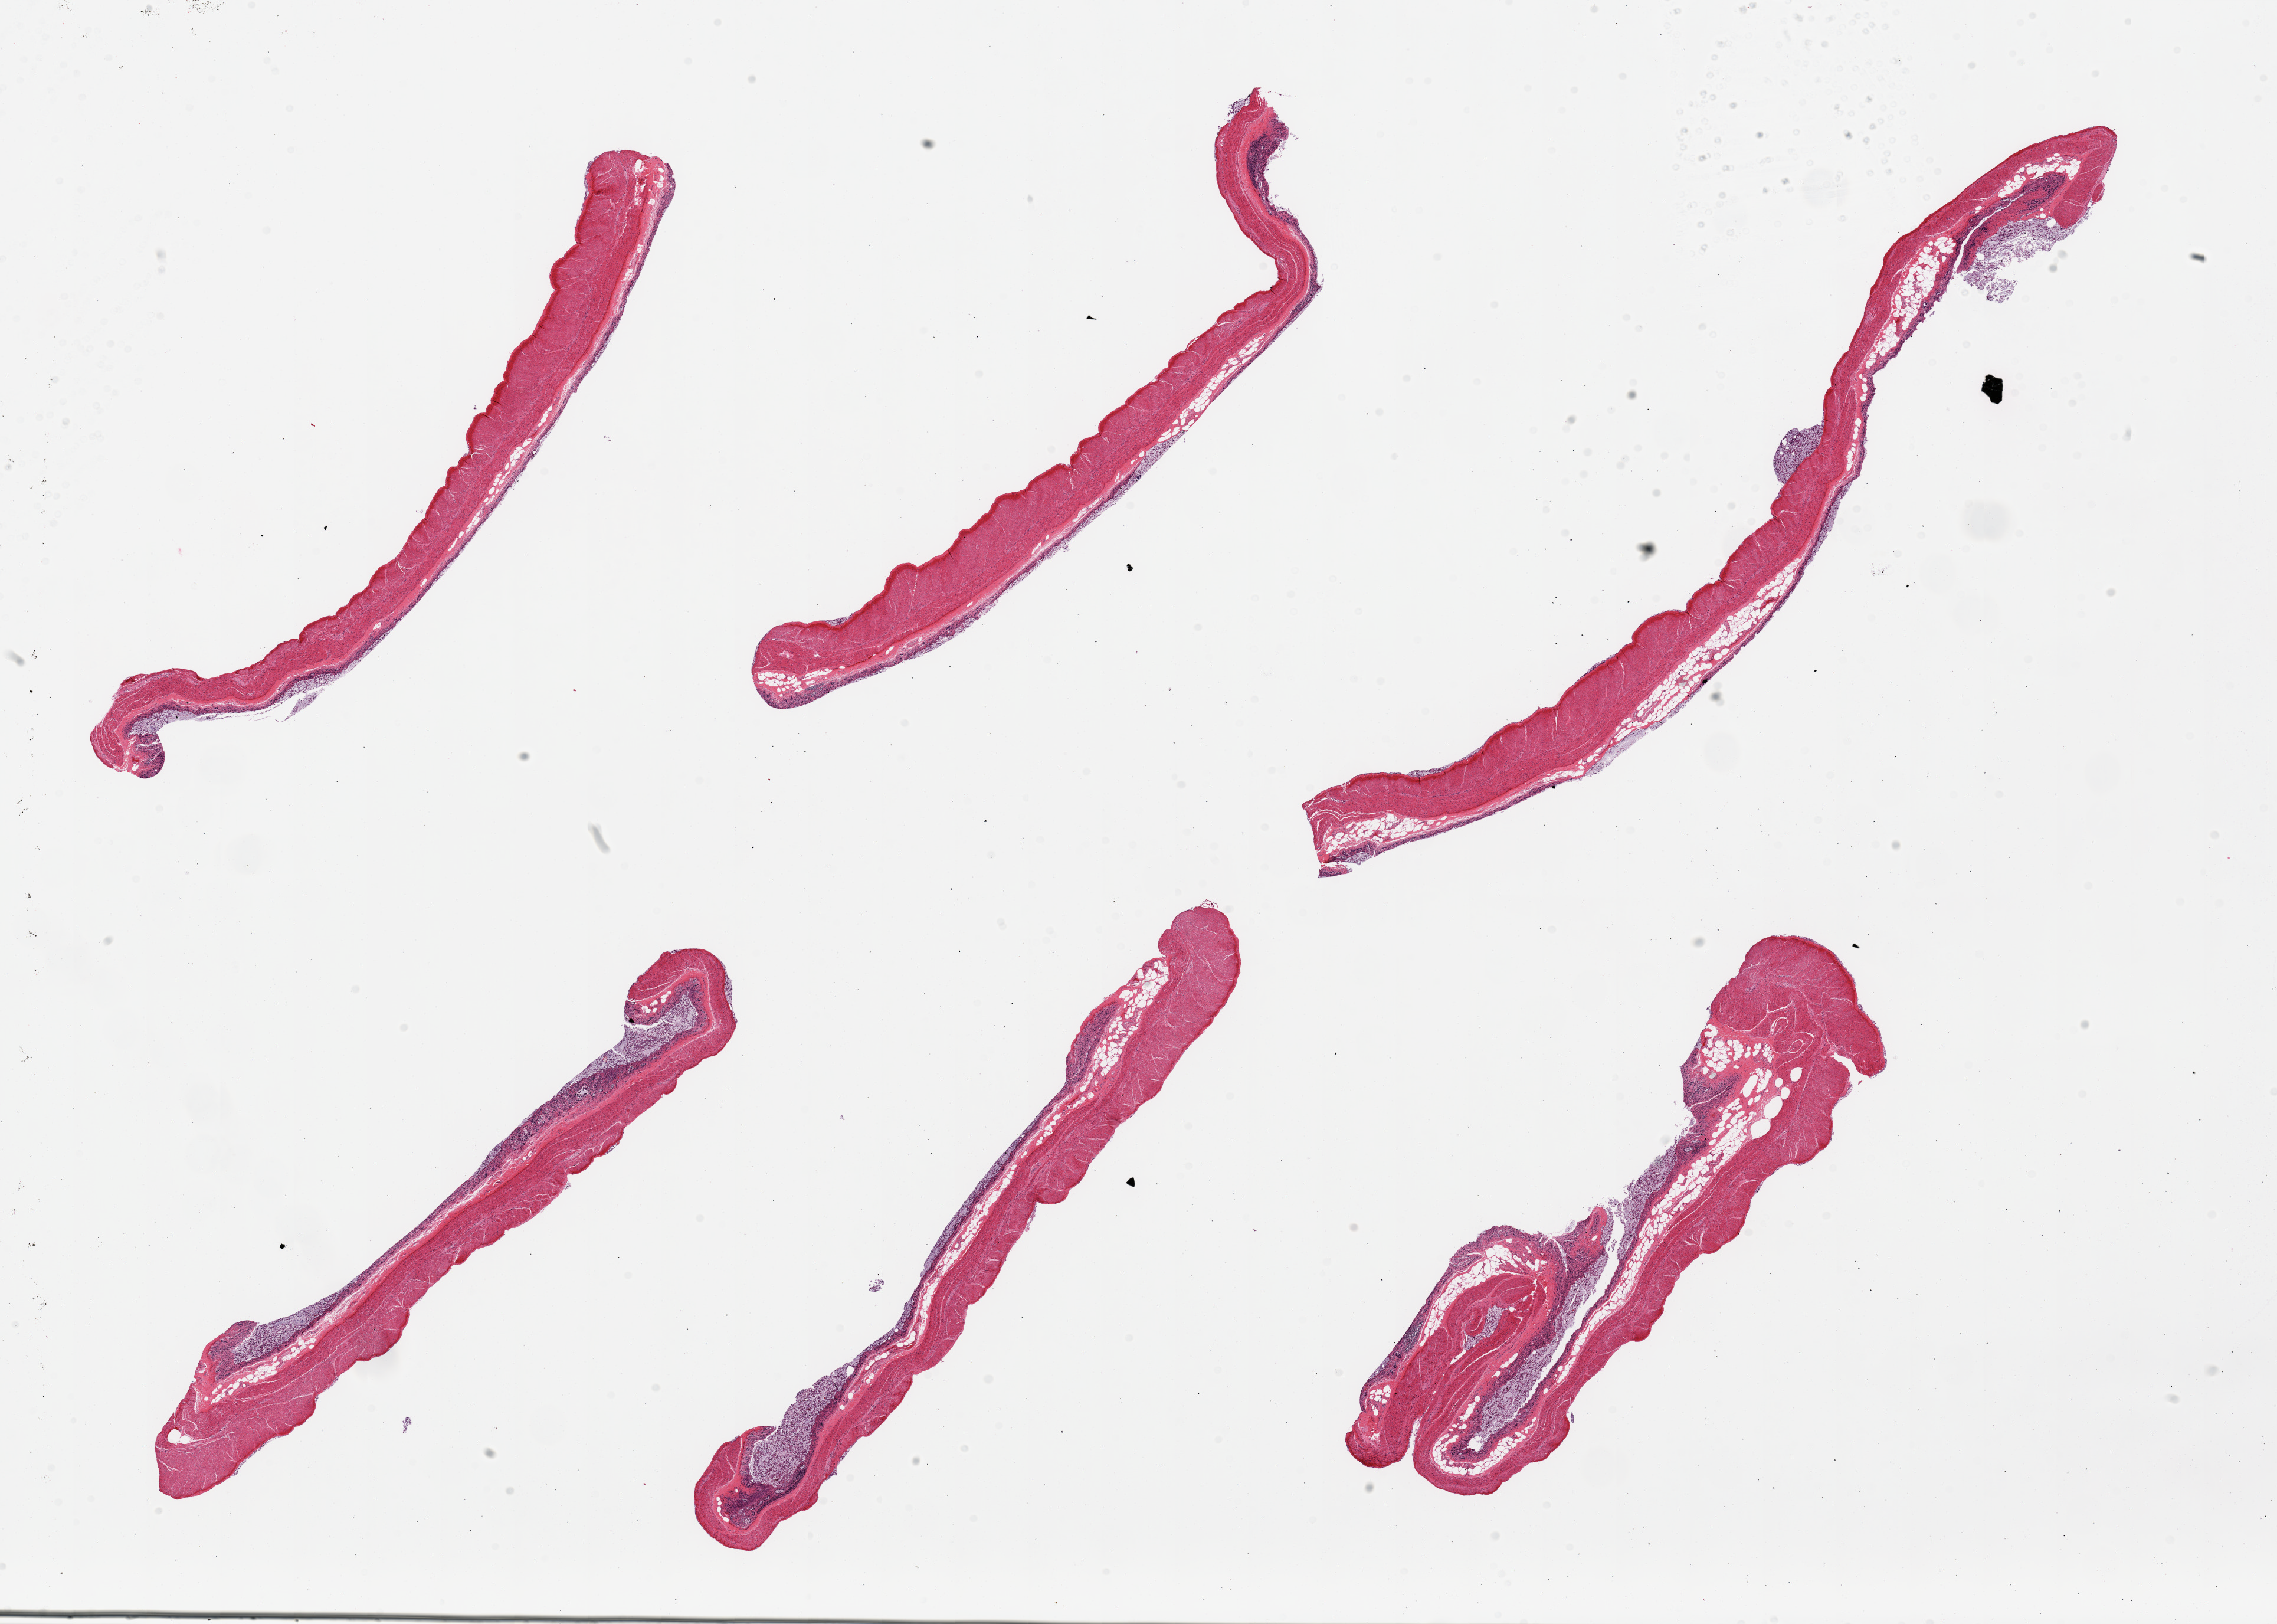
Digitized H&E-stained section, shown as a low-resolution overview of the whole scanned area (about 30.5 x 21.8 mm, slide scanned at 20x), PAXgene-fixed, paraffin-embedded tissue, sampled site (target tissue): sigmoid colon, tissue donor sample. Donor: male.
Reviewer comment on this tissue sample: 6 pieces, incudes autolyzed mucosa (not target, 3) and muscularis (1).